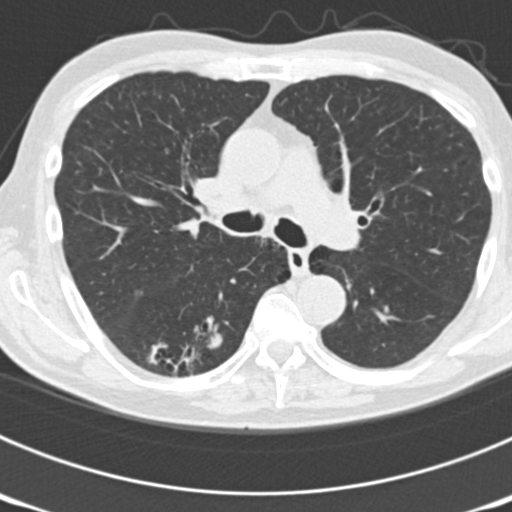
Chest CT (low-dose screening protocol), one axial image. Third annual screen. Lung window (W 1500 / L -600 HU). Slice 63 of 177 in the series. Male participant, aged 70 years at enrolment. Current smoker at enrolment.
• Expert reader's lesion annotation, bounding box (x1, y1, x2, y2) in pixels: (142, 312, 236, 386).
• The screening reader recorded 3 non-calcified nodules or masses ≥4 mm on this exam; which of them this box marks is not recorded.
• Participant outcome: lung cancer diagnosed 14 days after this screen — bronchiolo-alveolar adenocarcinoma, NOS, right lower lobe, poorly differentiated (G3), stage IB (AJCC 6th edition), 30 mm at pathology.